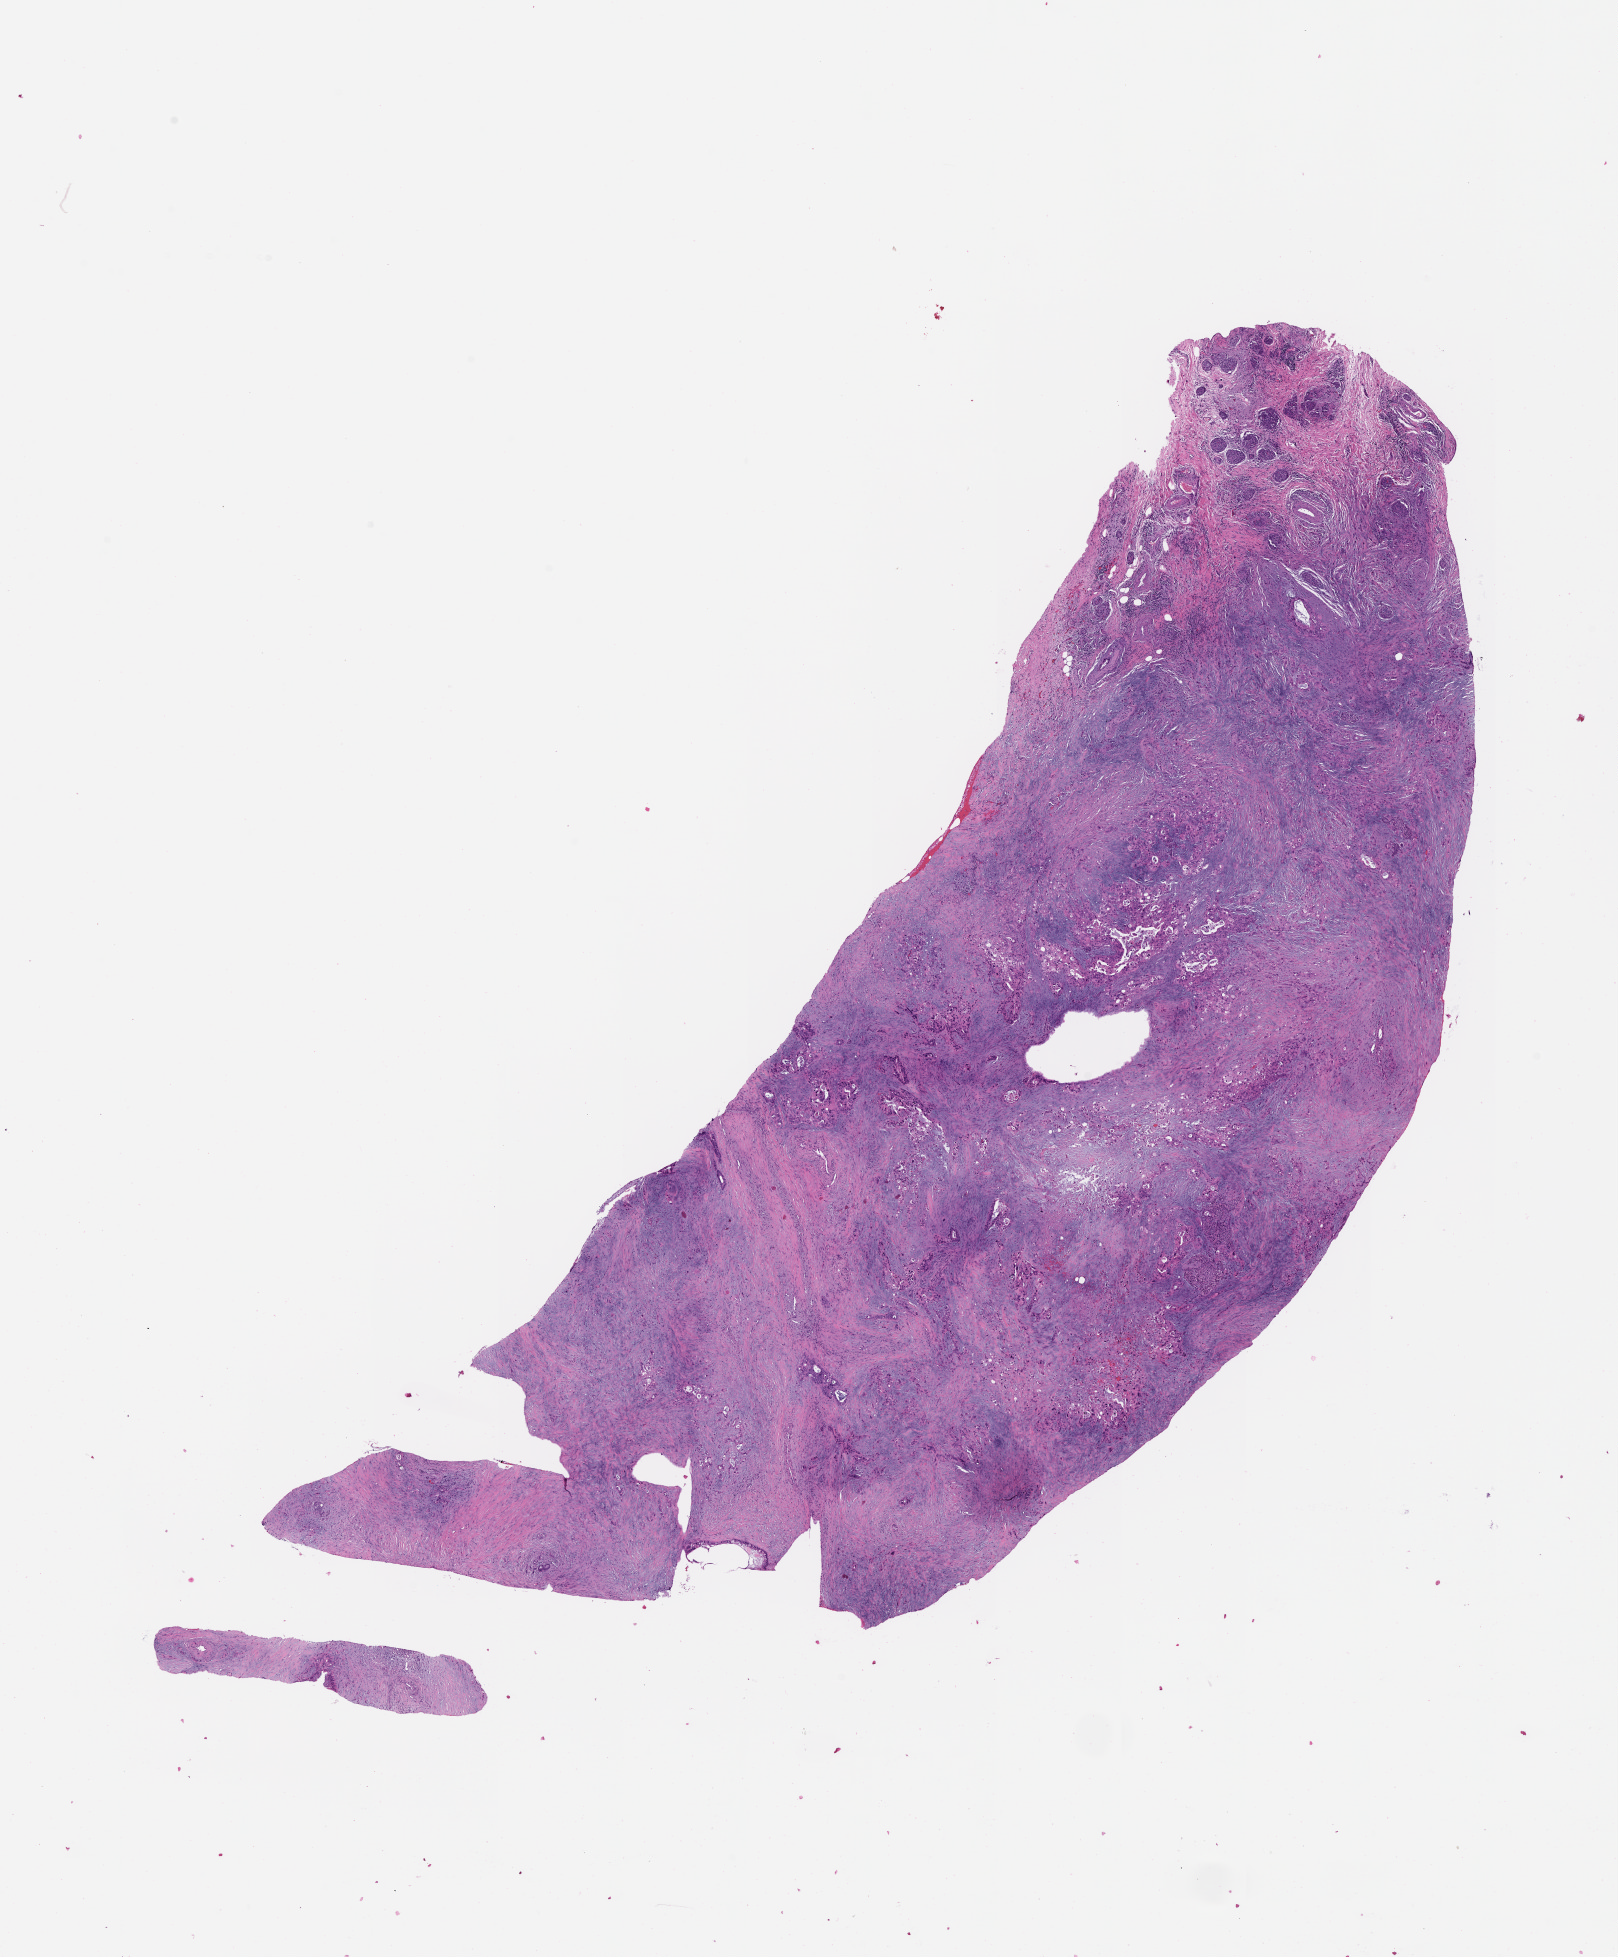
Digitized Hematoxylin and eosin (H&E) stained tissue section (whole slide) — whole scanned area (about 13.0 x 15.8 mm, acquisition: 20x scan) shown as a low-resolution overview; tumour tissue sample, sampled site: pancreas. Female, 71 y/o. Histologic grade: G3 (poorly differentiated). Pathologist review of this section (percent, as recorded): tumour nuclei 30%, necrosis 0%.
AJCC pathologic stage: IIB. Diagnosis: Infiltrating duct carcinoma, NOS. Primary tumour site (as recorded): head.